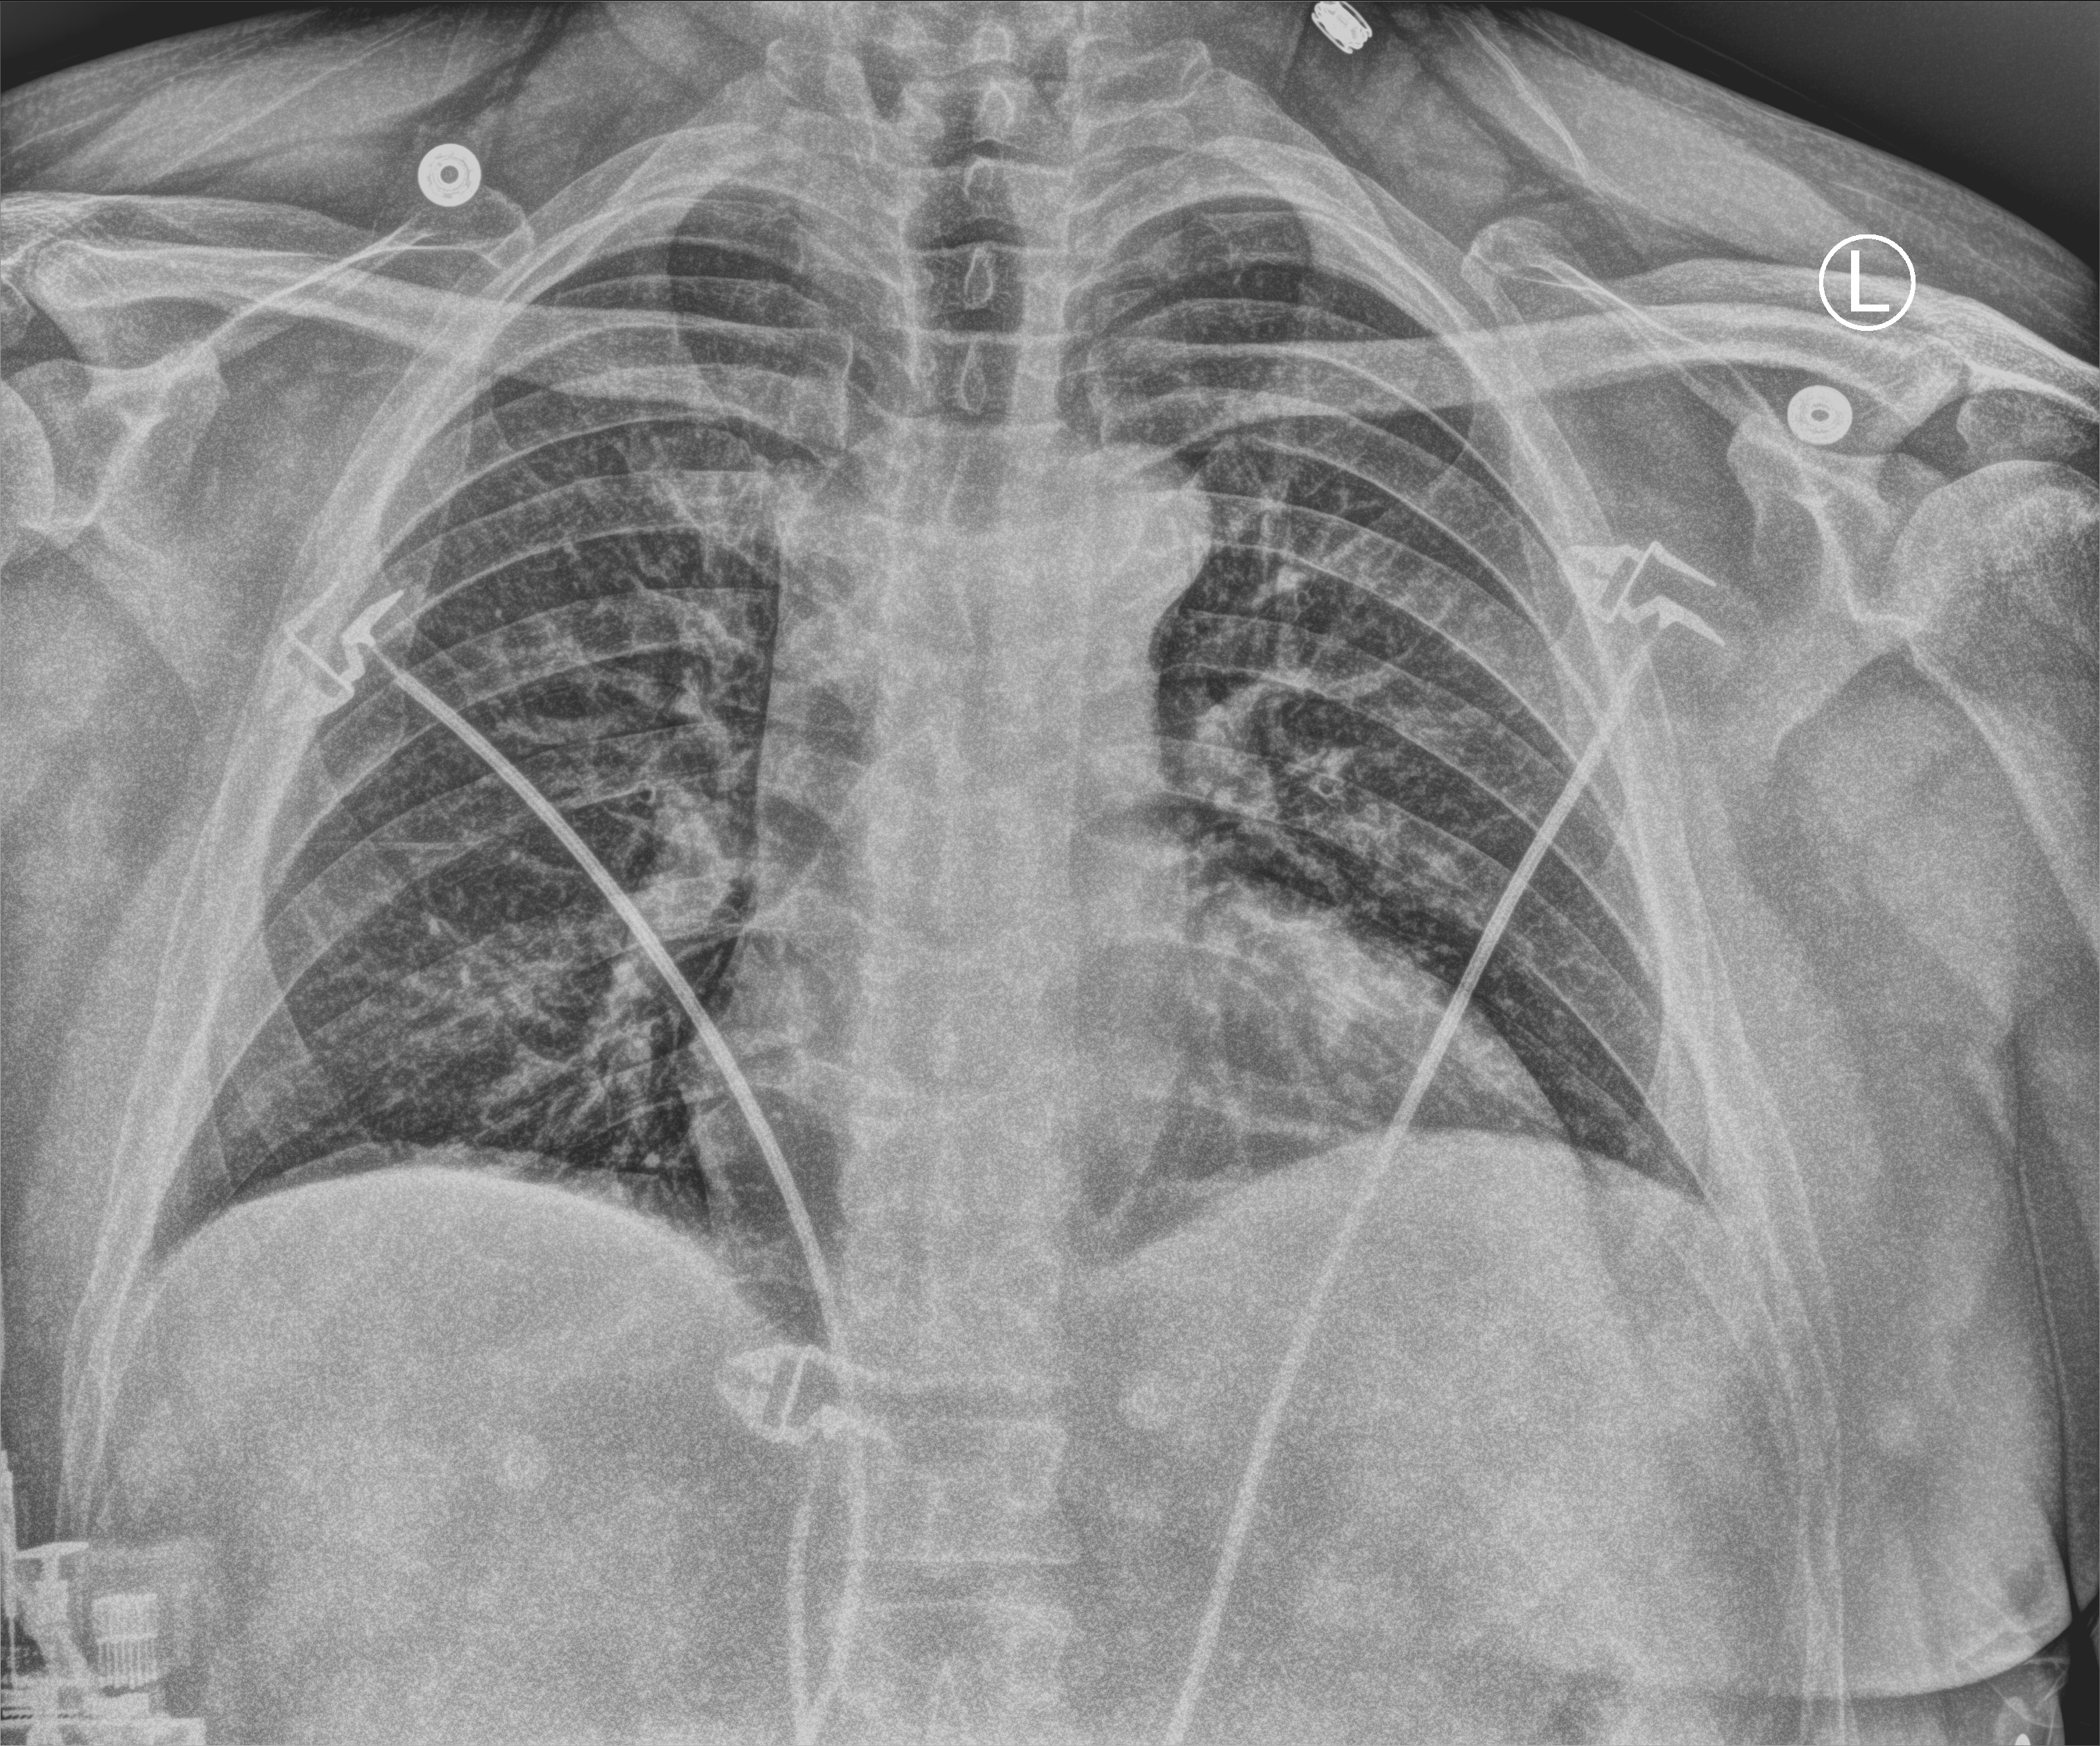
Portable chest radiograph, anteroposterior (AP) projection. Male patient hospitalised with COVID-19, age 18–59 years.
From the hospital-stay record, not from the radiograph (when in the stay this image was taken is not recorded):
- length of hospital stay: 6 days
- other chronic lung disease (admission record): yes